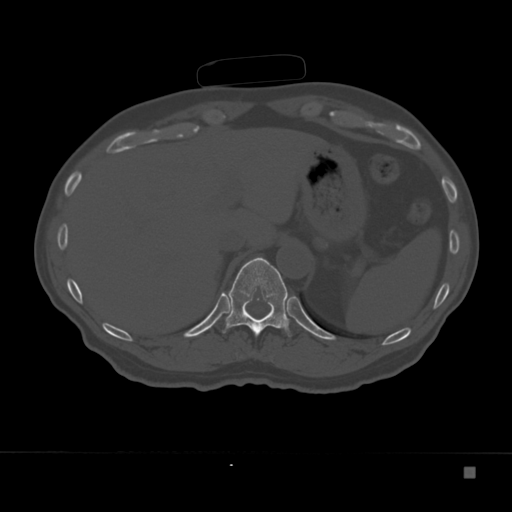
CT including the spine, one axial slice. Bone window (W 1800 / L 400 HU). 512 × 512 image matrix, field of view 389 × 389 mm. Patient: male, 72 years. Case-level facts recorded for this patient, not image findings: primary cancer: skeletal.
Outlined on this slice (semi-automatic segmentation, software-assisted and operator-edited):
- T11 vertebra: bounding box (x1, y1, x2, y2) in pixels: (222, 257, 291, 337)